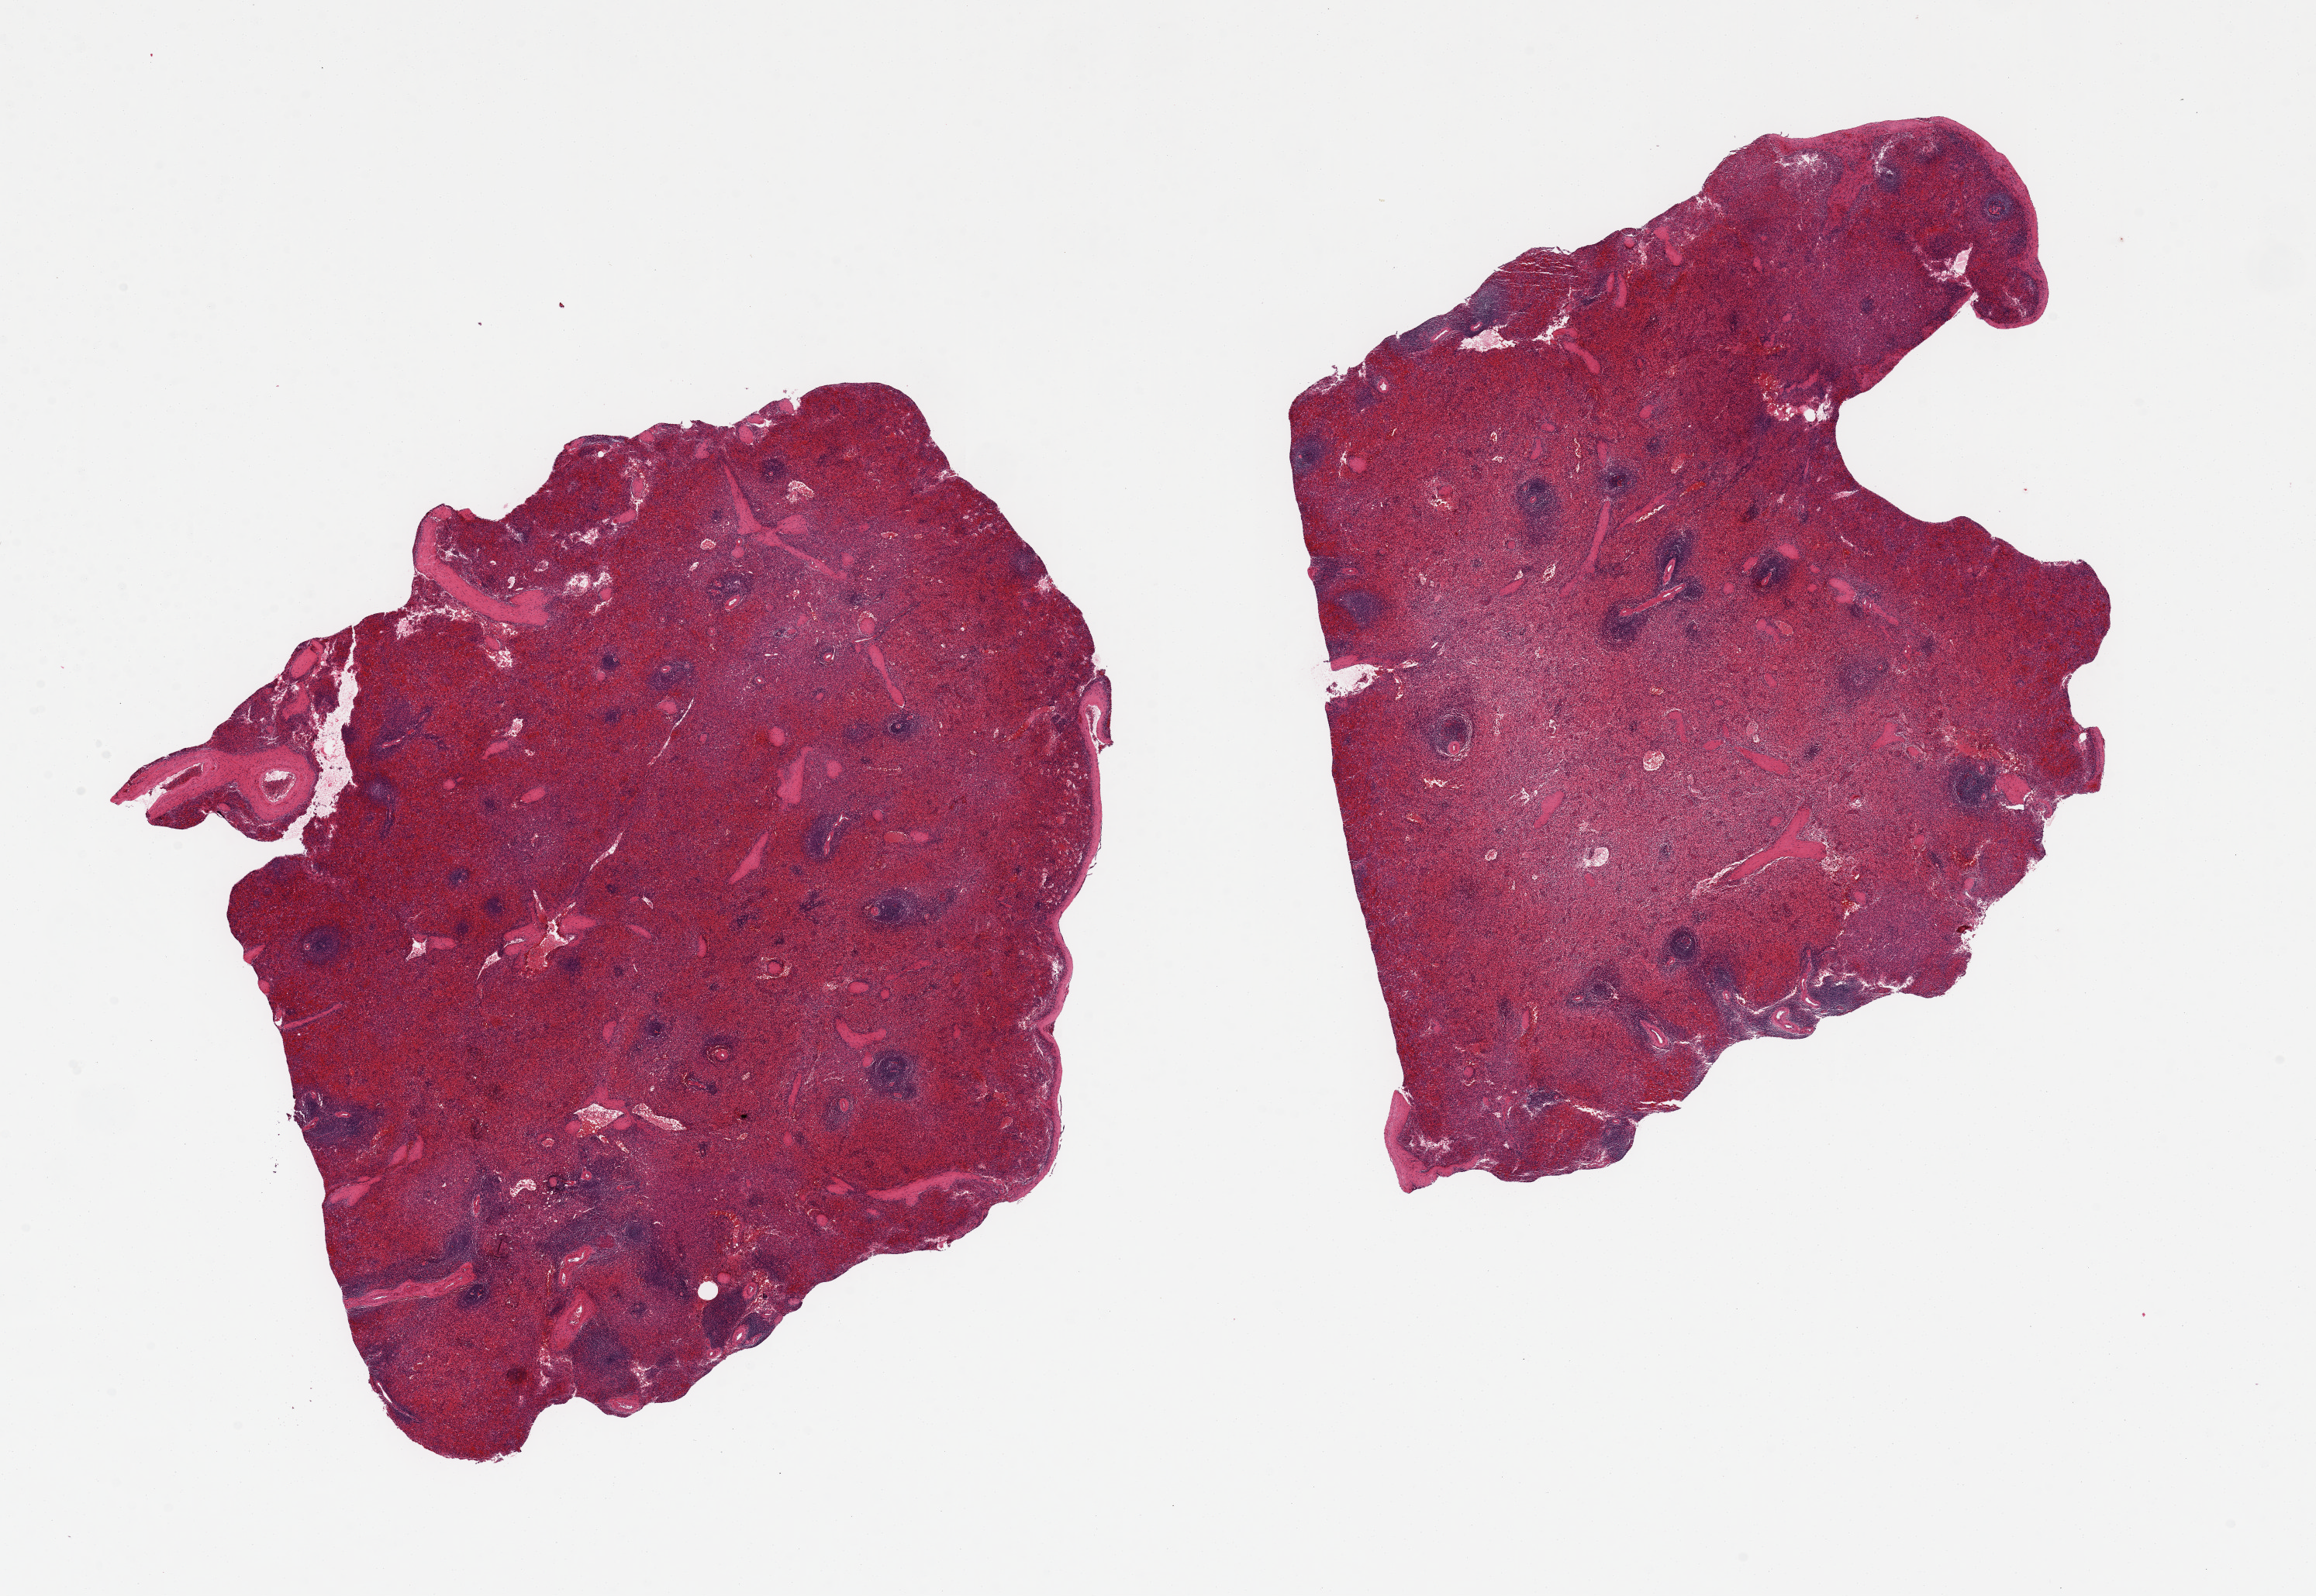
Digitized hematoxylin and eosin (H&E)-stained section — shown as a low-resolution overview of the whole scanned area (about 23.6 x 16.3 mm, slide scanned at 20x), PAXgene-fixed, paraffin-embedded tissue, target tissue: spleen, tissue donor sample.
Pathologist's review note for this sample: 2 pieces ~9x9mm.